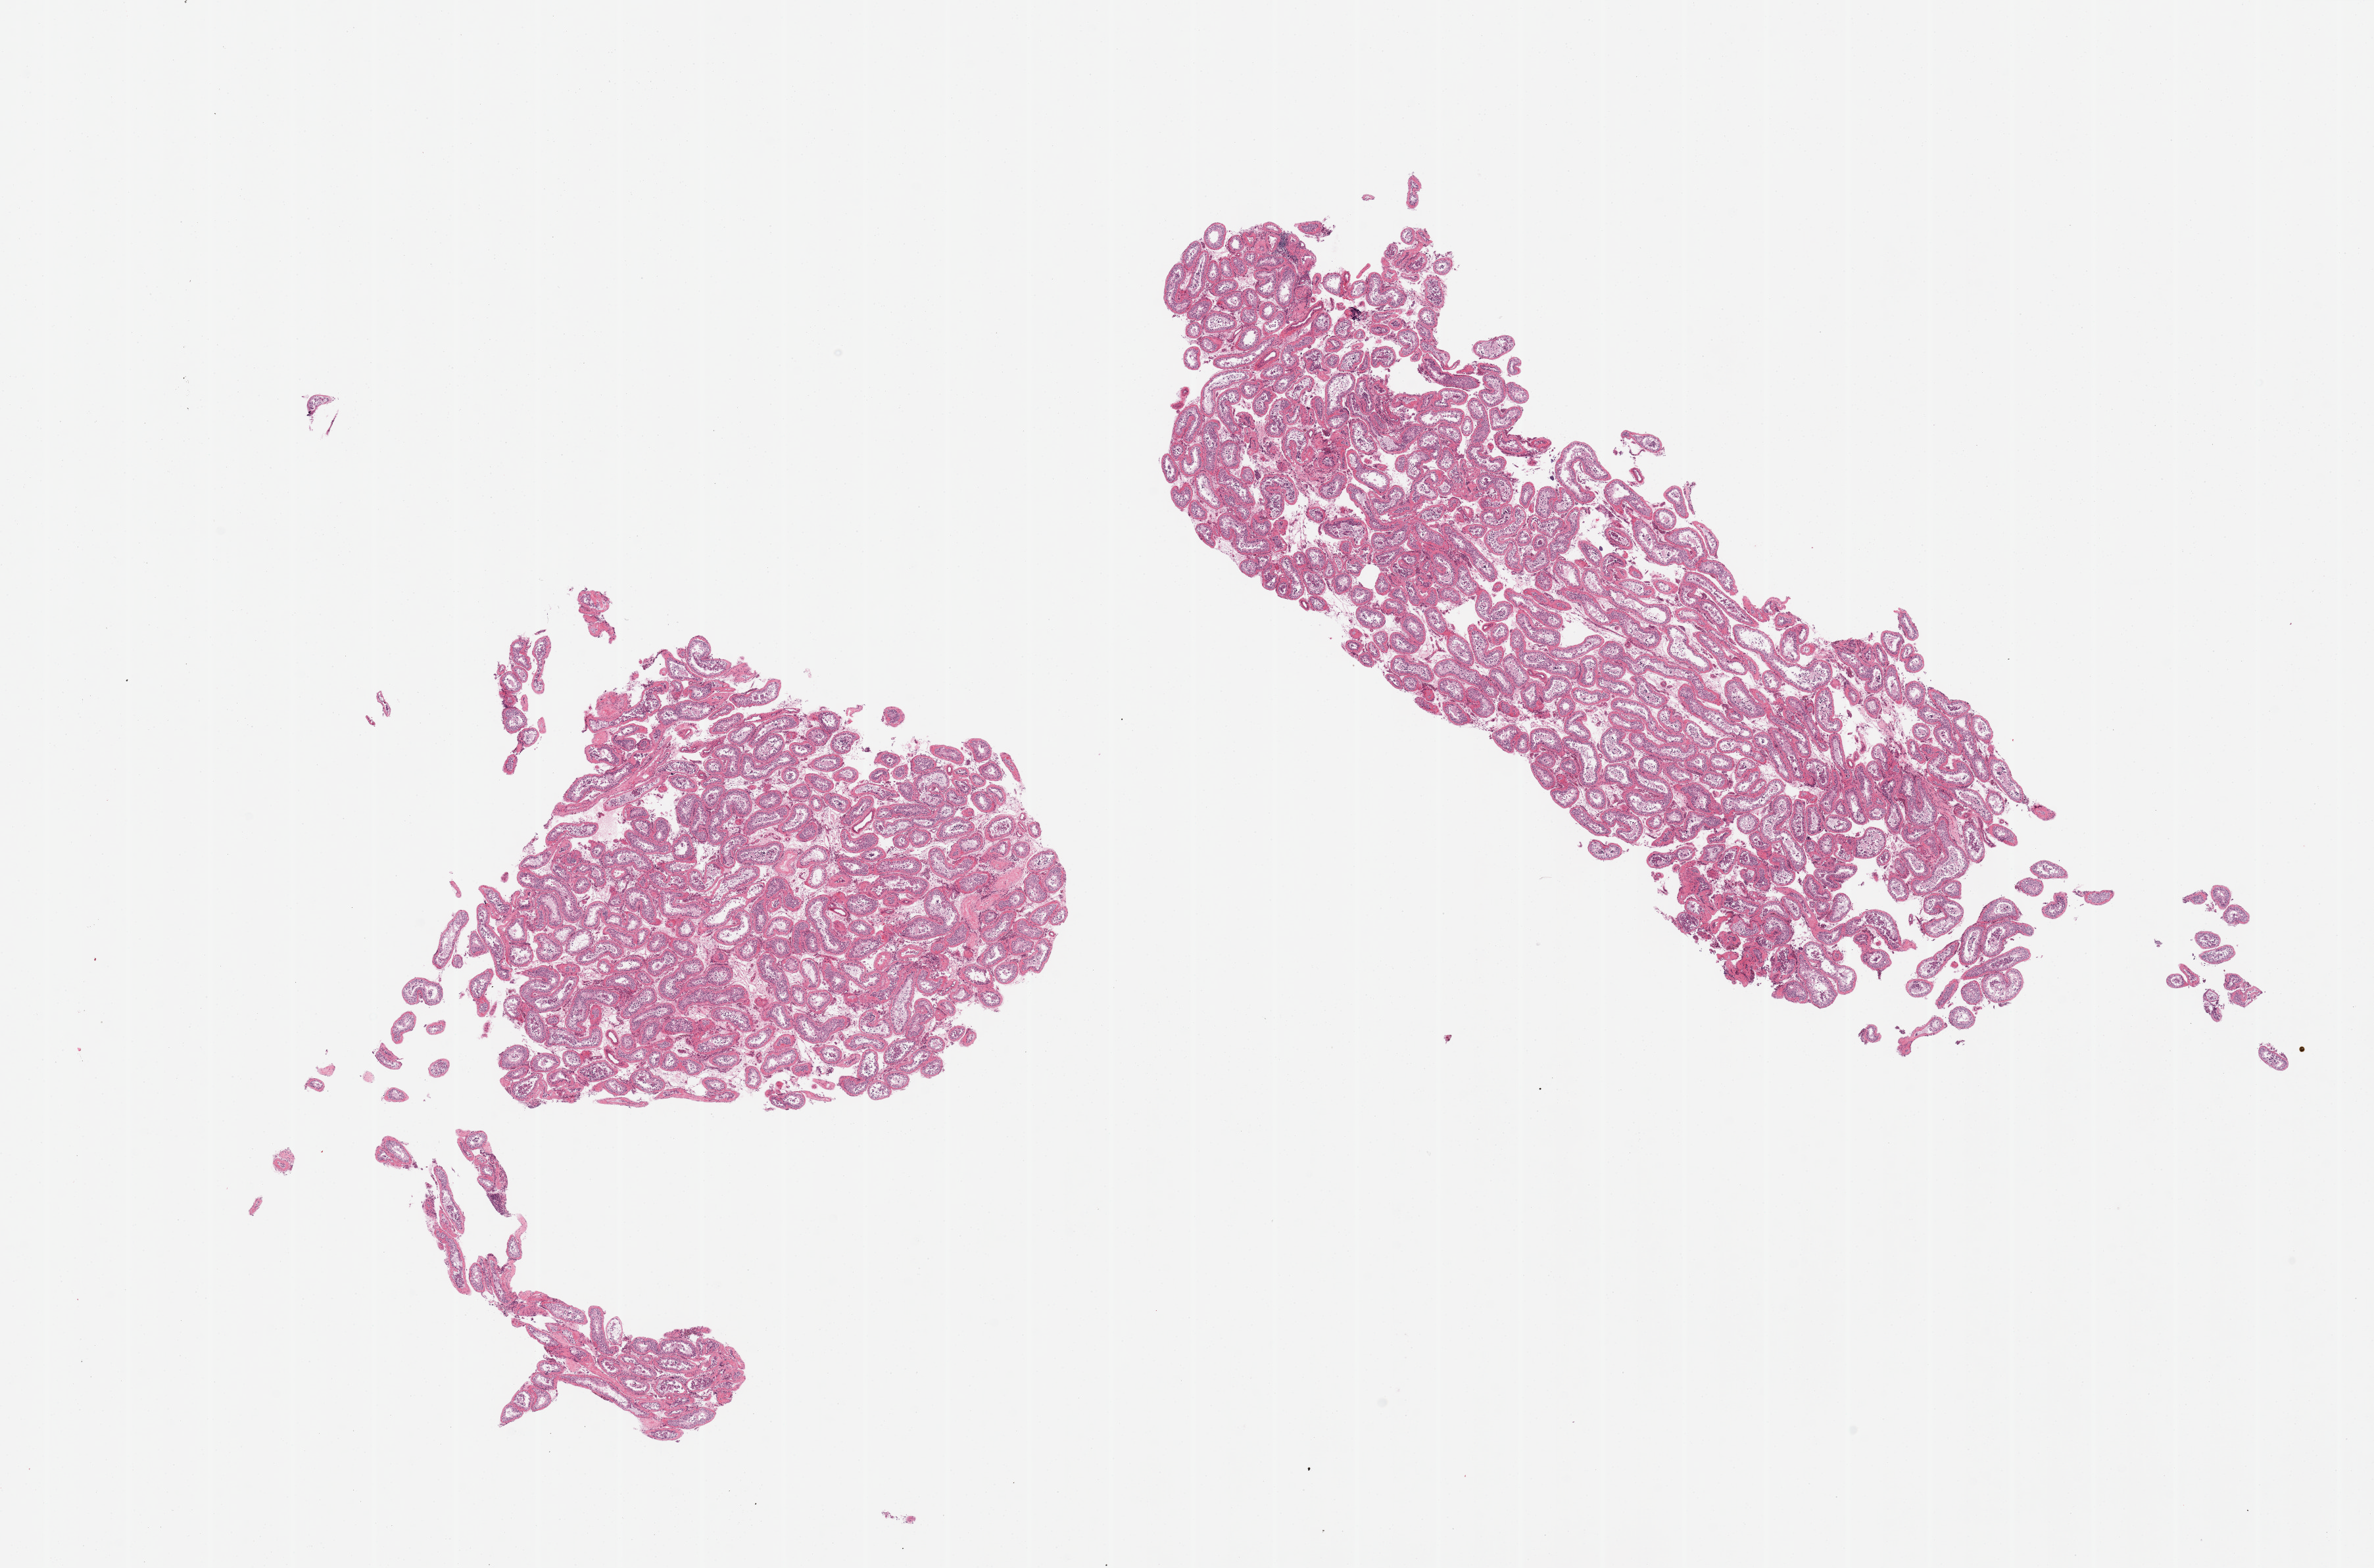
Digitized hematoxylin and eosin (H&E)-stained section, shown as a low-resolution overview of the whole scanned area (about 28.5 x 18.9 mm). PAXgene-fixed paraffin-embedded (PFPE) section. Sampled site (target tissue): testis. Tissue donor sample. Donor: male.
* reviewer comment on this tissue sample: 2 pieces; spermatogenesis